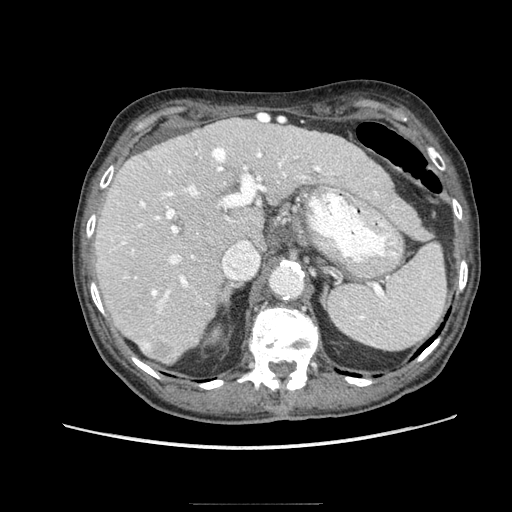
Contrast-enhanced abdominal CT (liver protocol), one axial slice. Position 56 of 83 along the scan axis. 140 kVp. Soft-tissue window (W 400 / L 40 HU). 2.5 mm slice thickness. 512 × 512 image matrix, field of view 360 × 360 mm. From the clinical record (not read from this slice): diagnosis: hepatocellular carcinoma (patient treated with transarterial chemoembolisation; whether this scan precedes or follows treatment is not stated here); TNM stage (as recorded): Stage-I; Child-Pugh class: A; tumour differentiation: moderately differentiated; tumour nodularity: uninodular.
Structures marked on this image (semi-automatically segmented with operator editing):
- liver parenchyma outside the tumour (the mass and vessels are separate outlines, so this box may not span the whole liver): bounding box (x1, y1, x2, y2) in pixels: (94, 118, 402, 361)
- mass: (139, 336, 178, 364)
- liver vessels: (100, 118, 395, 313)